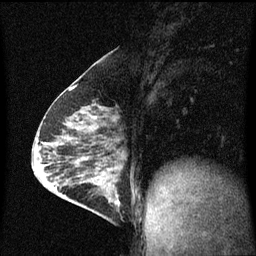
Breast MRI (dynamic contrast-enhanced), one sagittal slice; dynamic contrast-enhanced series, image 2 of 3 at this slice position (ordered by acquisition); 1.5 T; TE 4.2 ms, TR 8 ms; 2 mm slice thickness; 256 × 256 image matrix, field of view 200 × 200 mm. Patient: female, 64 years.
Outlined on this slice (semi-automatically segmented with operator editing):
- analysis volume of interest (the breast-tissue region the enhancement analysis was run in; not a lesion): bounding box (x1, y1, x2, y2) in pixels: (87, 176, 122, 217)
- tumour enhancement mask (voxels above the 70 % enhancement threshold inside the analysis volume of interest): (93, 180, 120, 209)